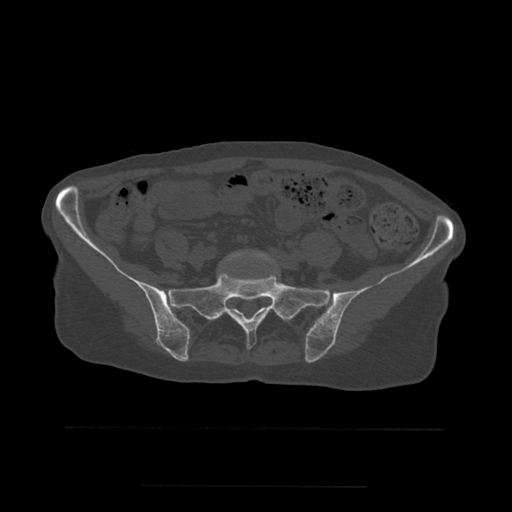
CT including the spine, one axial slice. Bone window (W 1800 / L 400 HU). 1.25 mm slice thickness. 512 × 512 image matrix, field of view 350 × 350 mm. Patient age 58 years. From the clinical record (not read from this slice): primary cancer: lung.
Outlined on this slice (semi-automatically segmented with operator editing):
- L5 vertebra: bounding box (x1, y1, x2, y2) in pixels: (224, 251, 274, 268)